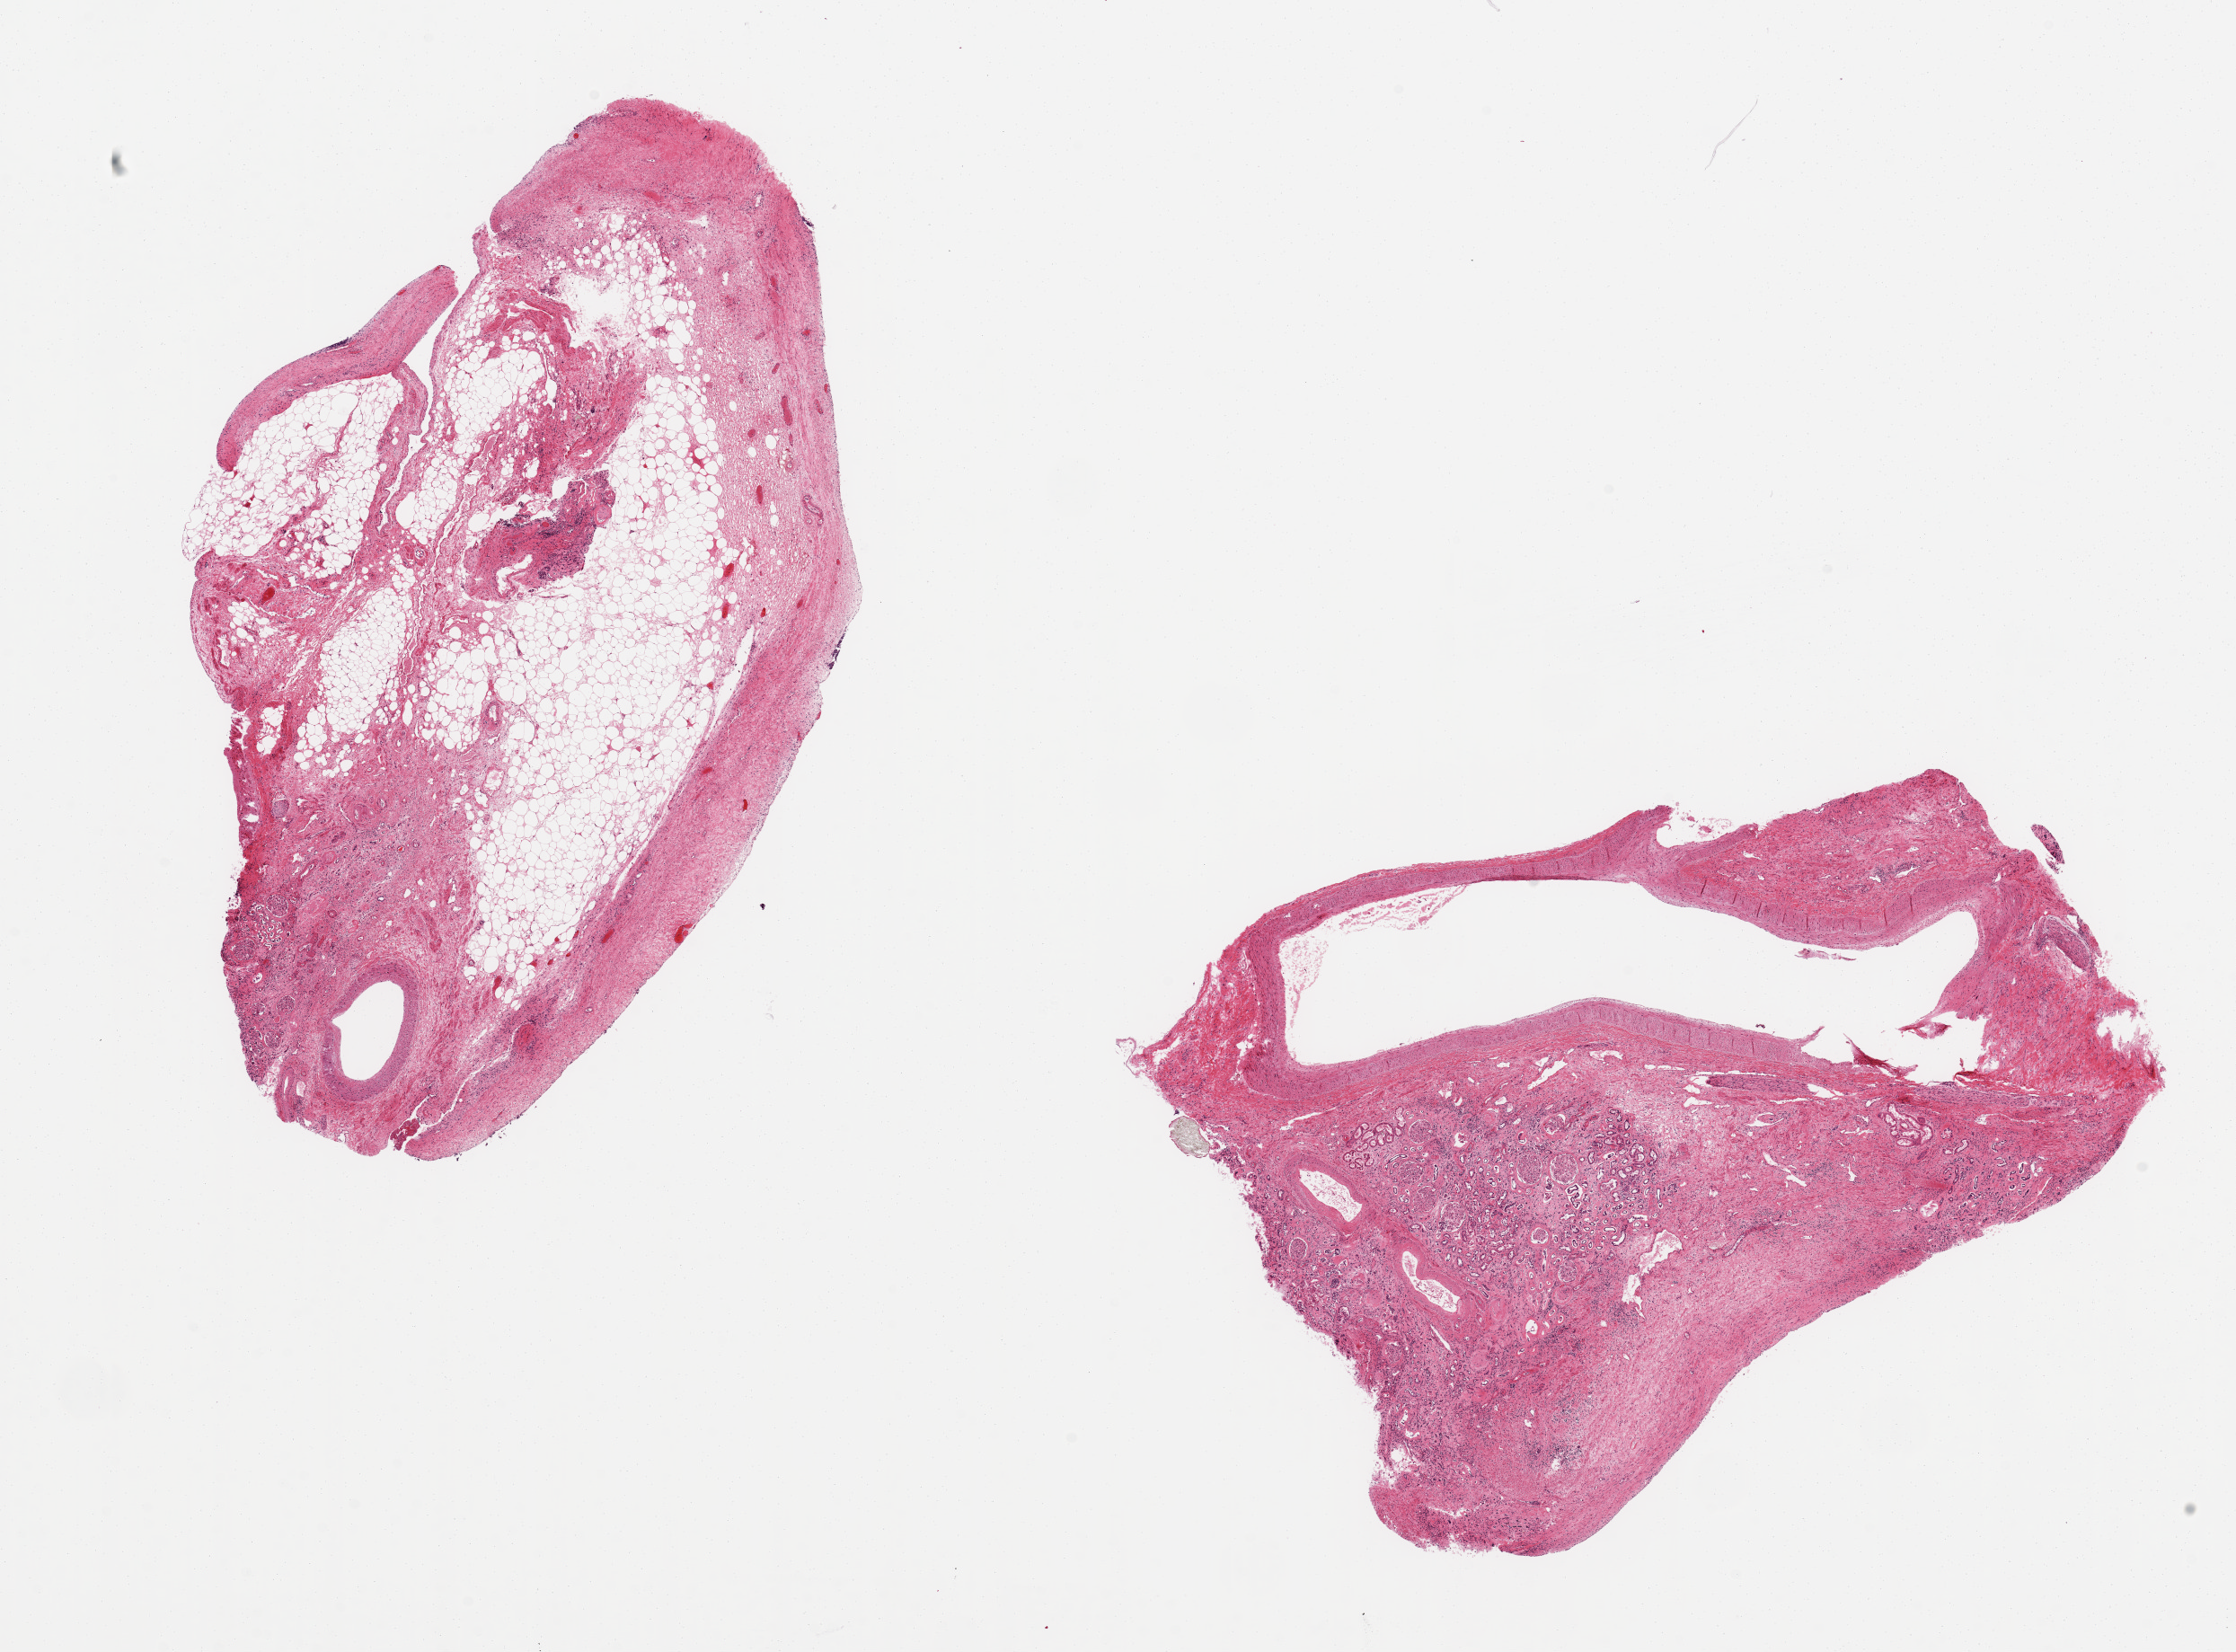
Hematoxylin and eosin (H&E) whole-slide image, shown as a low-resolution overview of the whole scanned area (about 19.7 x 14.5 mm, slide scanned at 20x); PAXgene-fixed paraffin-embedded (PFPE) section; sampled site (target tissue): renal medulla; donor tissue sample. Donor: male.
Review note (as recorded): 2 aliquots, one all fat/fibrovascular tissue, one vessel + small focus completely autozlyzed renal tubules.